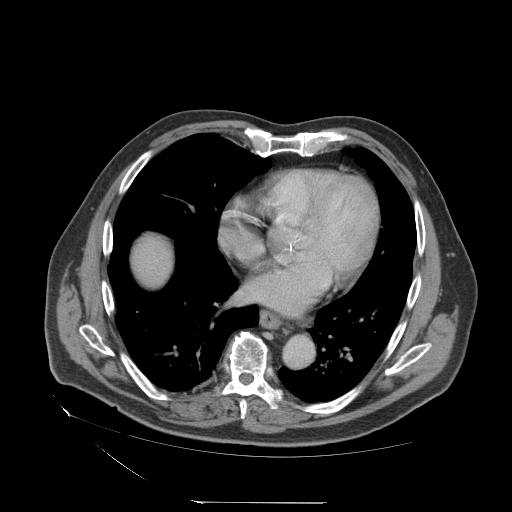
Contrast-enhanced abdominal CT (liver protocol), one axial slice. Slice 75 of 83 in the series (ordered by position). Reconstruction kernel STANDARD. 140 kVp. Soft-tissue window (W 400 / L 40 HU). 512 × 512 image matrix. Case-level facts recorded for this patient, not image findings: diagnosis: hepatocellular carcinoma (patient treated with transarterial chemoembolisation; whether this scan precedes or follows treatment is not stated here); TNM stage (as recorded): Stage-I; Child-Pugh class: A; tumour differentiation: well differentiated; tumour nodularity: uninodular.
Structures marked on this image (semi-automatically segmented with operator editing):
- liver parenchyma outside the tumour (the mass and vessels are separate outlines, so this box may not span the whole liver): box from (x=132, y=238) to (x=172, y=286) px